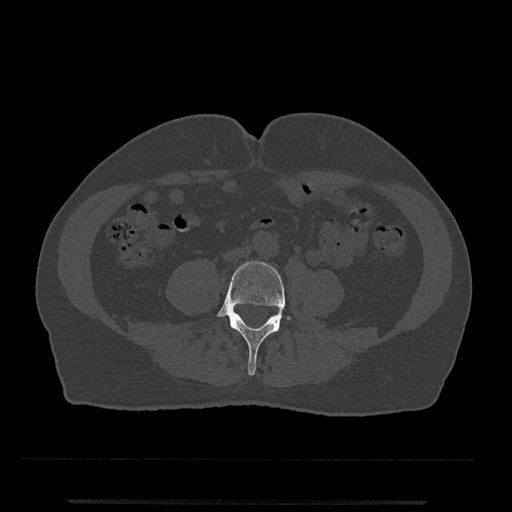
CT including the spine, one axial slice; reconstruction kernel Br40s/3; bone window (W 1800 / L 400 HU); 0.5 mm slice thickness; 512 × 512 image matrix, field of view 419 × 419 mm. Male patient, age 63 years. From the clinical record (not read from this slice): primary cancer: prostate.
Annotated regions visible in this slice (semi-automatically segmented with operator editing):
- L4 vertebra: bounding box (x1, y1, x2, y2) in pixels: (217, 260, 291, 376)